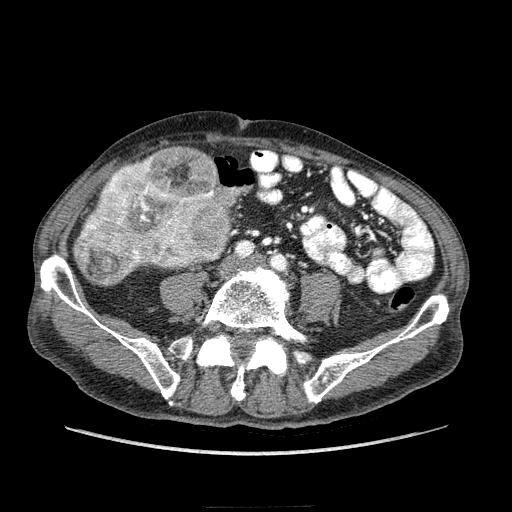
Contrast-enhanced abdominal CT (liver protocol), one axial slice; position 31 of 218 along the scan axis; 100 kVp; soft-tissue window (W 400 / L 40 HU); 512 × 512 image matrix, field of view 380 × 380 mm. Case-level facts recorded for this patient, not image findings: diagnosis: hepatocellular carcinoma (patient treated with transarterial chemoembolisation; whether this scan precedes or follows treatment is not stated here); TNM stage (as recorded): Stage-IIIA; Child-Pugh class: A; tumour differentiation: well differentiated.
Outlined on this slice (semi-automatically segmented with operator editing):
- mass: bounding box [x1, y1, x2, y2] px = [72, 146, 238, 286]